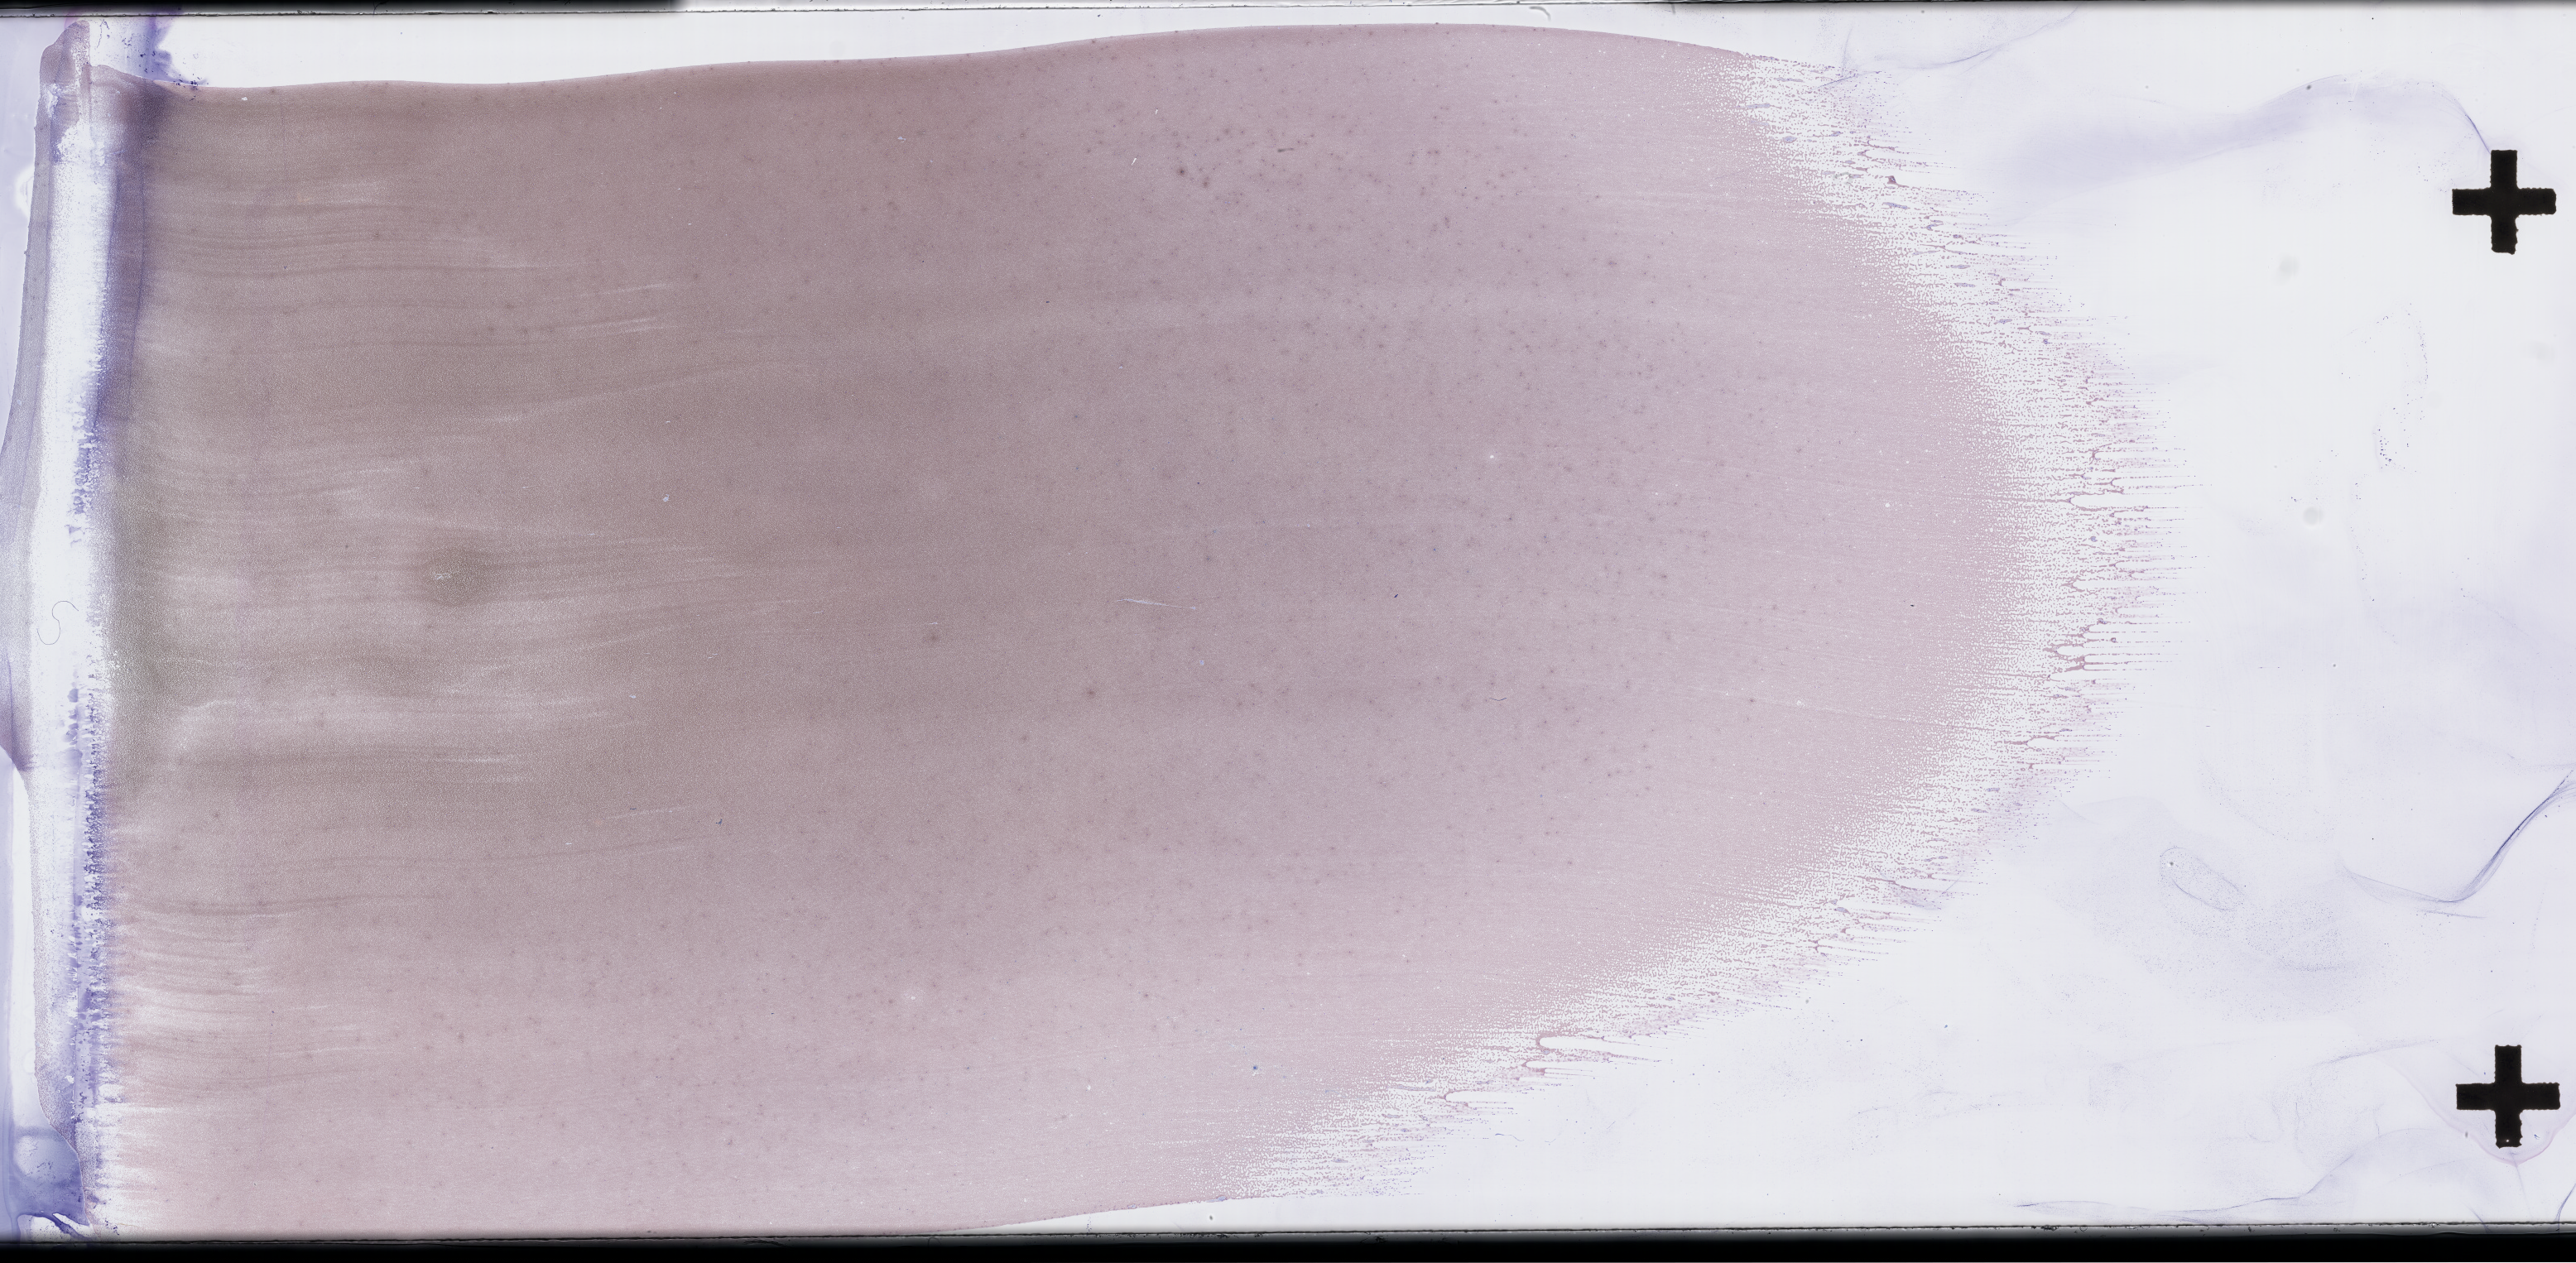
Wright–Giemsa-stained whole blood smear, whole-slide image — whole scanned area (about 50.3 x 24.6 mm) shown as a low-resolution overview. EDTA-anticoagulated smear. Specimen time point: collected on treatment. Male patient.
- patient diagnosis: Plasma Cell Myeloma